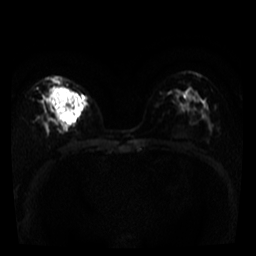
Breast MRI, one axial slice. Slice 22 of 39 in the series (ordered by position). Diffusion-weighted series; image 2 of 4 stored at this slice position (different b-values; order by instance number). 3 T. 5 mm slice thickness. 256 × 256 image matrix, field of view 280 × 280 mm. Female patient.
Structures marked on this image (outlined manually by an expert reader):
- tumour on diffusion-weighted imaging: bounding box (x1, y1, x2, y2) in pixels: (50, 86, 85, 126)